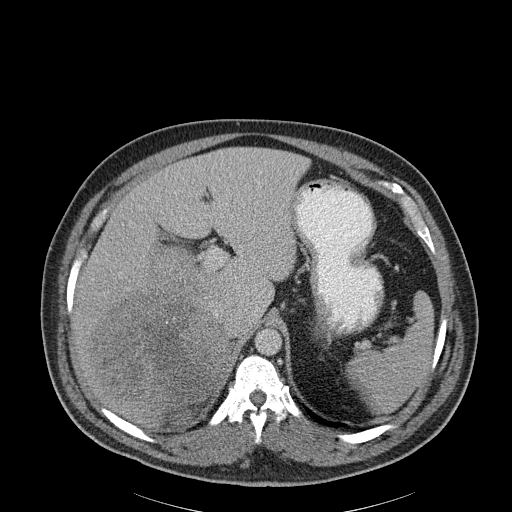
Contrast-enhanced abdominal CT, one axial slice; slice 144 of 186 in the series (ordered by position); 120 kVp; soft-tissue window (W 400 / L 40 HU); 512 × 512 image matrix, field of view 464 × 464 mm. Patient: male, 56 years. Case-level facts recorded for this patient, not image findings: diagnosis: adrenocortical carcinoma; tumour side: right adrenal; tumour size at pathology: 18 cm; Ki-67 index: 2 %; stage (as recorded): 3.
Structures marked on this image (semi-automatically segmented with operator editing):
- mass: bounding box <94,253,226,412> (left, top, right, bottom; pixels)